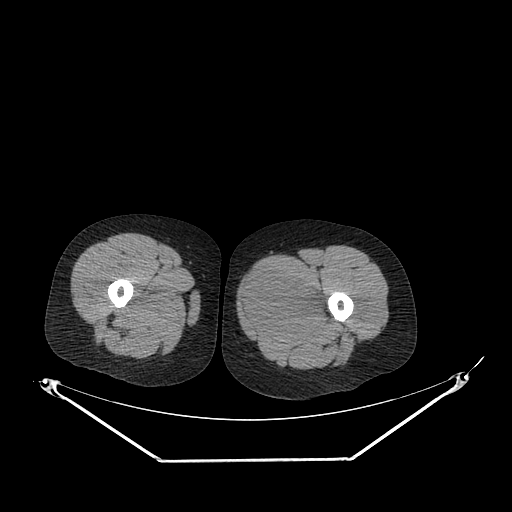
CT of an extremity soft-tissue mass (from a PET/CT study), one axial slice; slice 231 of 267 in the series (ordered by position); reconstruction kernel SOFT; 120 kVp; soft-tissue window (W 400 / L 40 HU); 3.75 mm slice thickness; 512 × 512 image matrix. Female patient. From the clinical record (not read from this slice): histological type: pleiomorphic leiomyosarcoma; grade: intermediate; site of the primary tumour: left thigh.
Annotated regions visible in this slice (expert contour drawn on MRI and transferred to this co-registered scan by the dataset authors):
- gross tumour volume including surrounding oedema: bounding box [x1, y1, x2, y2] px = [240, 267, 330, 334]
- gross tumour volume (mass): [242, 269, 323, 334]